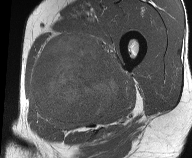
MRI of an extremity soft-tissue mass, one axial slice; slice 27 of 61 in the series (ordered by position); MR volume resampled by the dataset authors to the PET/CT grid (not the native acquisition matrix); 3.27 mm slice thickness; 192 × 158 image matrix, field of view 187 × 154 mm. Male patient. From the clinical record (not read from this slice): histological type: pleiomorphic liposarcoma; grade: high; site of the primary tumour: left thigh.
Annotated regions visible in this slice (expert contour drawn on MRI and transferred to this co-registered scan by the dataset authors):
- gross tumour volume including surrounding oedema: bounding box (x1, y1, x2, y2) in pixels: (29, 30, 128, 129)
- gross tumour volume (mass): (32, 35, 120, 122)